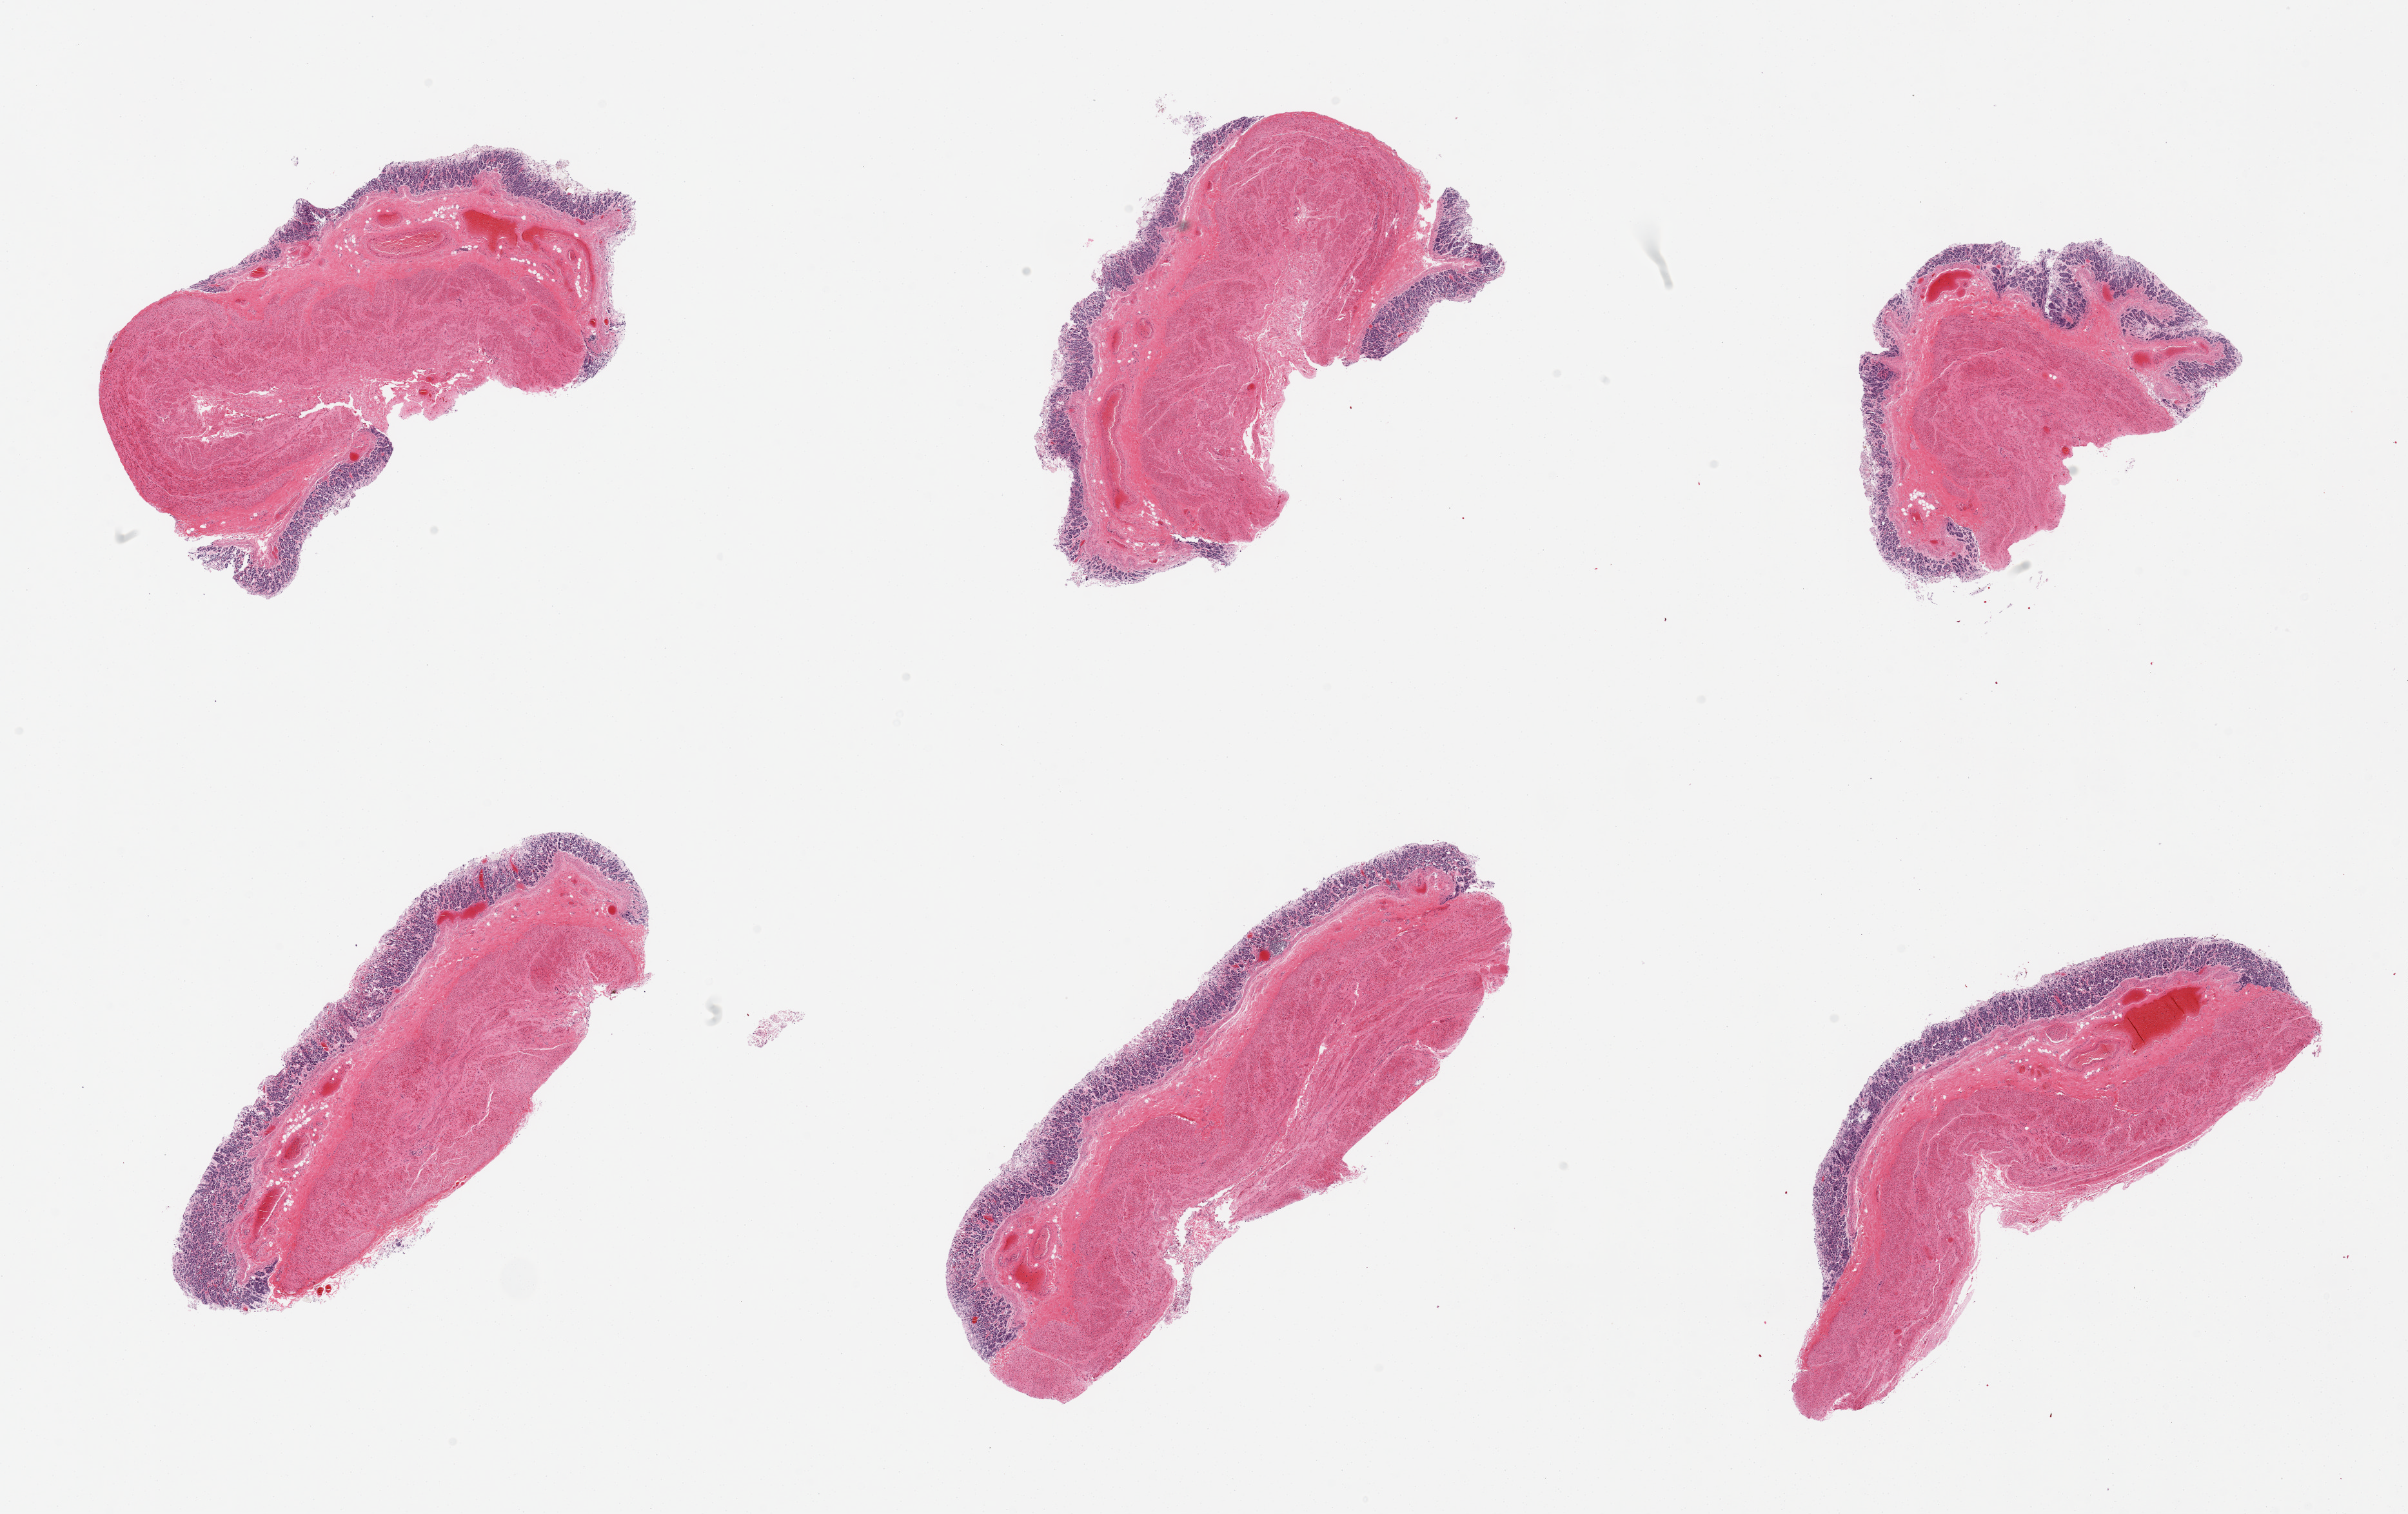
Haematoxylin and eosin whole-slide image — shown as a low-resolution overview of the whole scanned area (about 29.5 x 18.6 mm). PAXgene-fixed, paraffin-embedded tissue. Sampled site (target tissue): stomach. Tissue donor sample. Male donor.
- review note (as recorded): 6 pieces, mucosa and muscularis